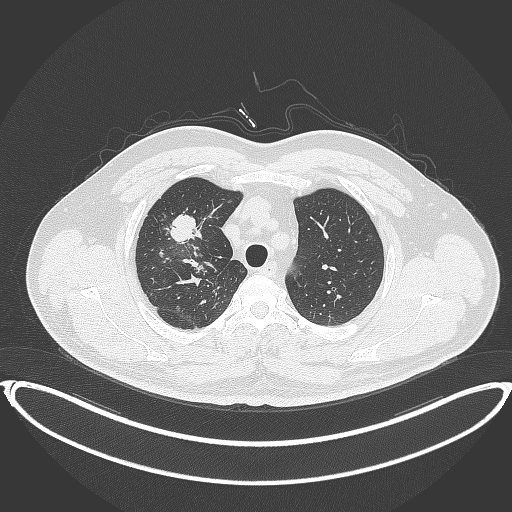
Chest CT, one axial slice; slice 307 of 399 in the series (ordered by position); reconstruction kernel B70f; 120 kVp; lung window (W 1500 / L -600 HU); 512 × 512 image matrix. Patient: male, 53 years. From the clinical record (not read from this slice): clinical TNM (as recorded): T2a N0 M0.
Outlined on this slice (bounding box drawn by a radiologist):
- lung tumour (recorded histology: adenocarcinoma): bounding box (x1, y1, x2, y2) in pixels: (163, 211, 205, 246)